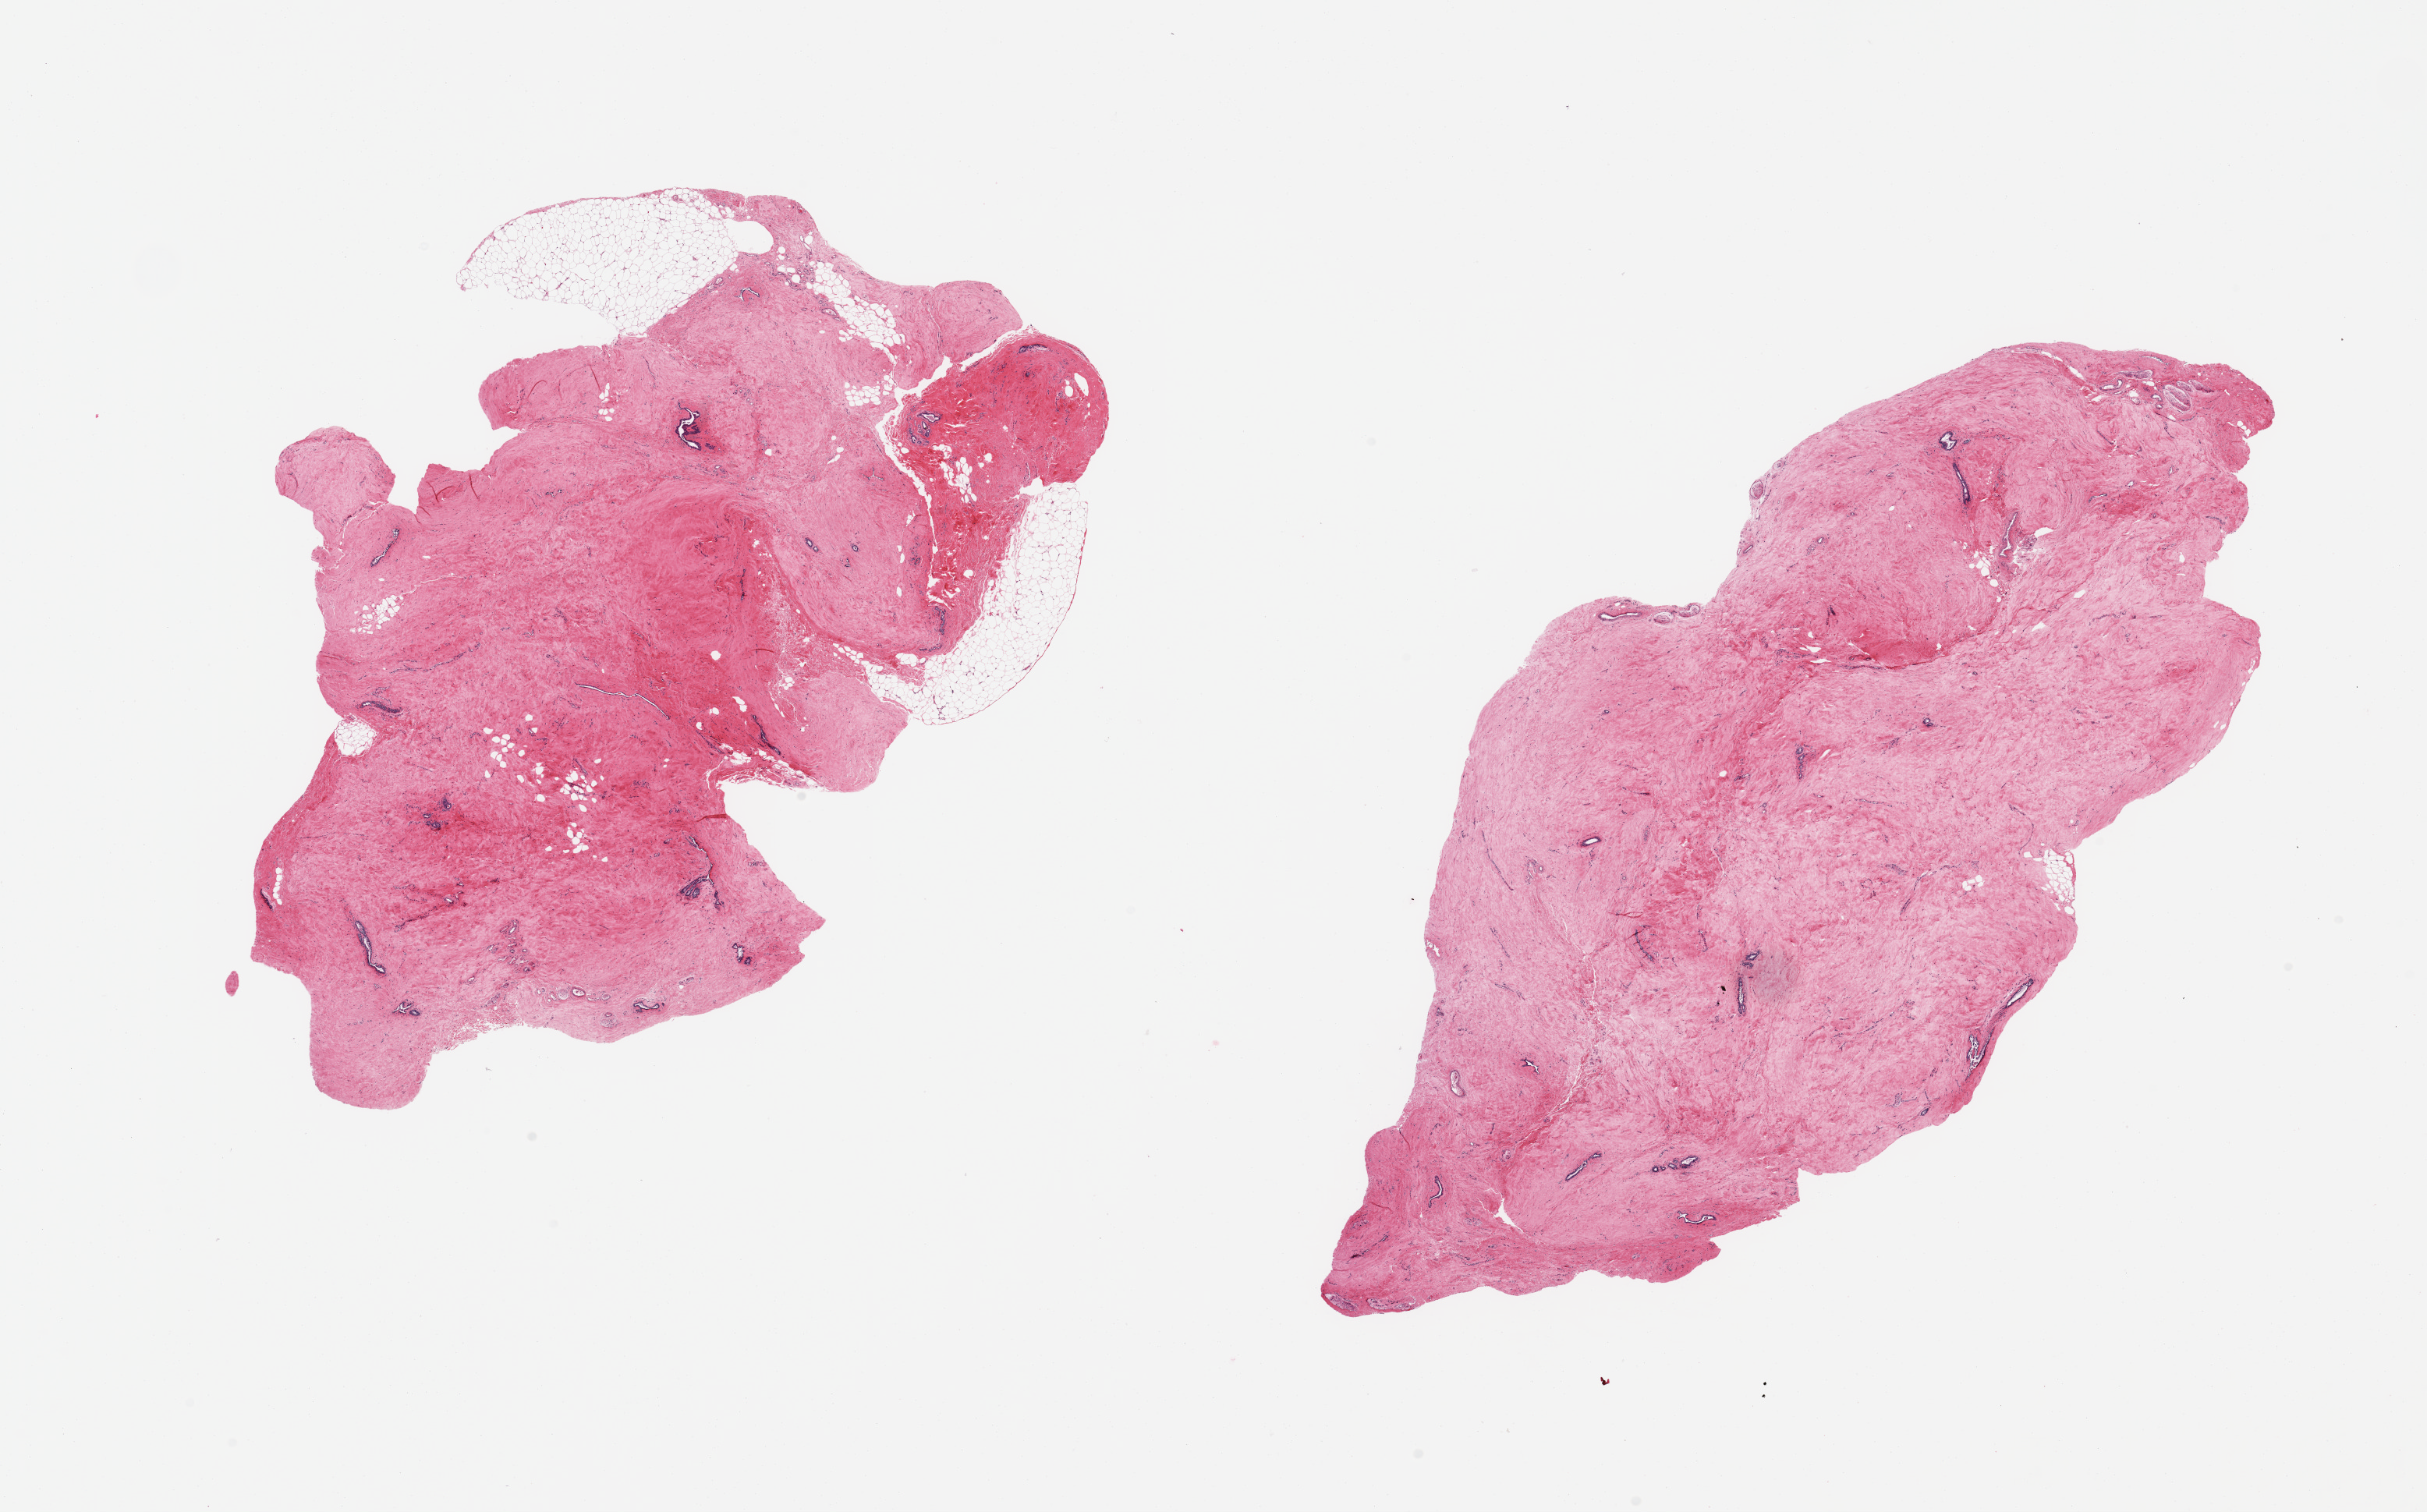
Digitized H&E-stained section — whole scanned area (about 24.6 x 15.3 mm, slide scanned at 20x) shown as a low-resolution overview, PAXgene-fixed, paraffin-embedded tissue, target tissue: breast, tissue donor sample. Donor: male.
• review note (as recorded): 2 pieces; gynecomastoid hyperplasia